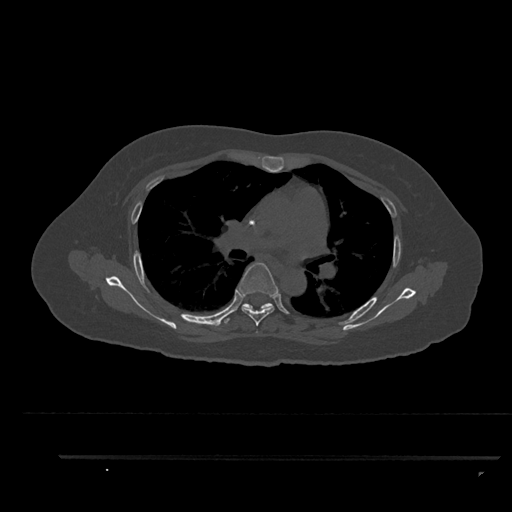
CT including the spine, one axial slice. Position 588 of 797 along the scan axis. Reconstruction kernel Br40s/3. 120 kVp. Bone window (W 1800 / L 400 HU). 0.5 mm slice thickness. 512 × 512 image matrix, field of view 408 × 408 mm. Female patient, age 44 years. From the clinical record (not read from this slice): primary cancer: renal.
Annotated regions visible in this slice (semi-automatically segmented with operator editing):
- T4 vertebra: bounding box (x1, y1, x2, y2) in pixels: (256, 331, 258, 333)
- T5 vertebra: (239, 262, 278, 326)
- T6 vertebra: (226, 303, 273, 323)